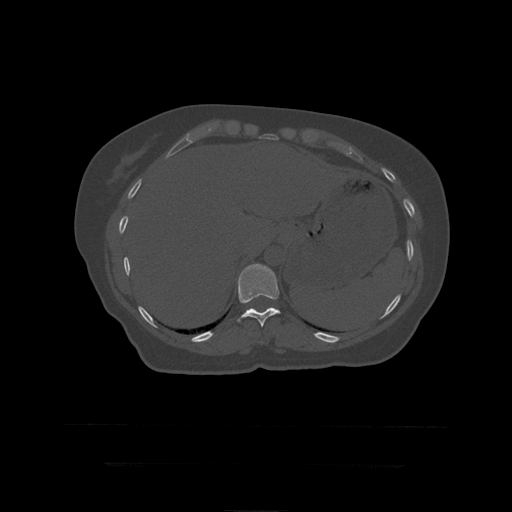
CT including the spine, one axial slice. Bone window (W 1800 / L 400 HU). 1.25 mm slice thickness. 512 × 512 image matrix, field of view 450 × 450 mm. Patient age 41 years. Case-level facts recorded for this patient, not image findings: primary cancer: breast.
Annotated regions visible in this slice (semi-automatic segmentation, software-assisted and operator-edited):
- T11 vertebra: bounding box (x1, y1, x2, y2) in pixels: (237, 264, 281, 328)